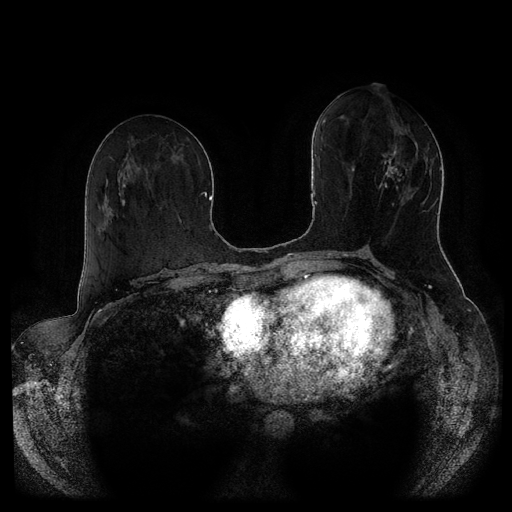
Breast MRI (dynamic contrast-enhanced, multi-phase), one axial slice; position 45 of 116 along the scan axis; dynamic contrast-enhanced series, time point 2 of 5 at this slice position (early post-contrast); 1.5 T; TE 2.6 ms, TR 5.3 ms; 2 mm slice thickness; 512 × 512 image matrix, field of view 370 × 370 mm. Patient: female, 51 years.
Structures marked on this image (semi-automatically segmented with operator editing):
- breast lesion (labelled 'tumour' in the annotation; benign lesions carry a separate 'benign' label): bounding box [x1, y1, x2, y2] px = [375, 146, 408, 206]